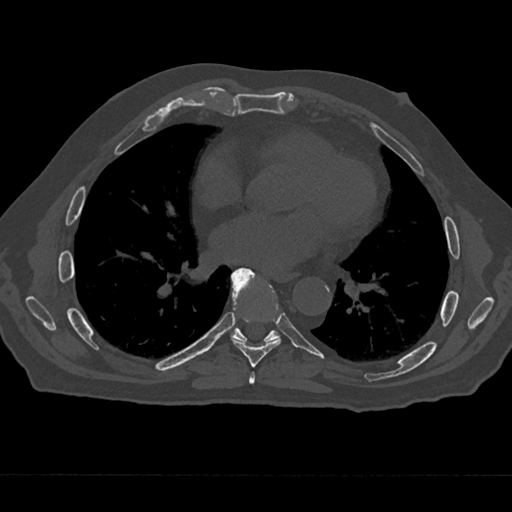
CT including the spine, one axial slice; slice 350 of 797 in the series (ordered by position); 120 kVp; bone window (W 1800 / L 400 HU); 0.5 mm slice thickness; 512 × 512 image matrix. Male patient, age 75 years. Case-level facts recorded for this patient, not image findings: primary cancer: renal.
Annotated regions visible in this slice (semi-automatic segmentation, software-assisted and operator-edited):
- T6 vertebra: bounding box (x1, y1, x2, y2) in pixels: (249, 372, 255, 385)
- T7 vertebra: (231, 267, 282, 368)
- T8 vertebra: (230, 274, 280, 343)